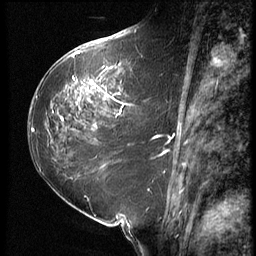
Breast MRI (dynamic contrast-enhanced), one sagittal slice; slice 32 of 64 in the series (ordered by position); 3 images stored at this slice position (order not interpretable as contrast timing); 1.5 T; TE 4.2 ms, TR 9 ms; 2.5 mm slice thickness; 256 × 256 image matrix, field of view 180 × 180 mm. Patient: female, 59 years. From the clinical record (not read from this slice): setting: breast cancer imaged before/during neoadjuvant chemotherapy; receptor status: HER2-positive.
Structures marked on this image (semi-automatic segmentation, software-assisted and operator-edited):
- analysis volume of interest (the breast-tissue region the enhancement analysis was run in; not a lesion): box from (x=54, y=65) to (x=155, y=132) px
- tumour enhancement mask (voxels above the 140 % enhancement threshold inside the analysis volume of interest): (x=63, y=65)–(x=133, y=121)